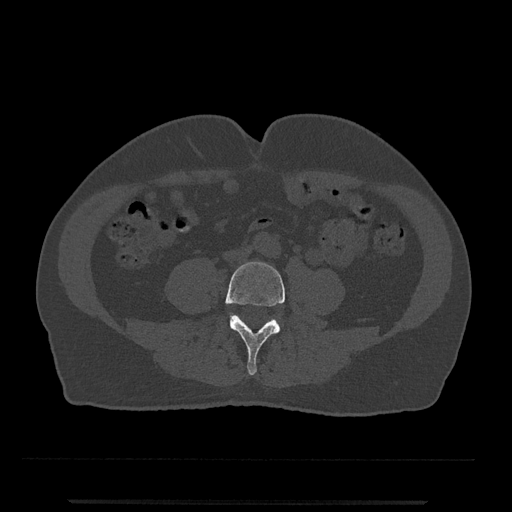
CT including the spine, one axial slice. Position 129 of 797 along the scan axis. Bone window (W 1800 / L 400 HU). 0.5 mm slice thickness. 512 × 512 image matrix, field of view 419 × 419 mm. Patient: male, 63 years. From the clinical record (not read from this slice): primary cancer: prostate.
Outlined on this slice (semi-automatically segmented with operator editing):
- L4 vertebra: bounding box (x1, y1, x2, y2) in pixels: (225, 261, 285, 375)
- L5 vertebra: (279, 325, 280, 331)